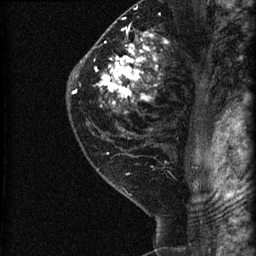
Breast MRI (dynamic contrast-enhanced), one sagittal slice. Position 47 of 60 along the scan axis. Dynamic contrast-enhanced series, image 2 of 3 at this slice position (ordered by acquisition). 1.5 T. TE 4.2 ms, TR 22.7 ms. 1.8 mm slice thickness. 256 × 256 image matrix, field of view 180 × 180 mm. Patient: female, 45 years. Case-level facts recorded for this patient, not image findings: setting: breast cancer imaged before/during neoadjuvant chemotherapy; receptor status: HR-positive, HER2-negative.
Structures marked on this image (semi-automatically segmented with operator editing):
- analysis volume of interest (the breast-tissue region the enhancement analysis was run in; not a lesion): box from (x=74, y=11) to (x=205, y=140) px
- tumour enhancement mask (voxels above the 90 % enhancement threshold inside the analysis volume of interest): (x=74, y=28)–(x=166, y=104)